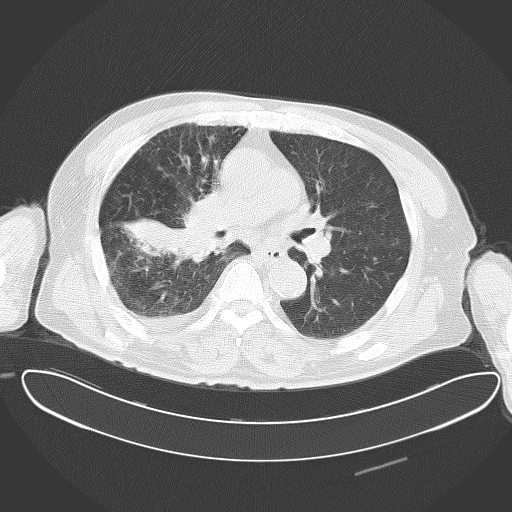
Chest CT, one axial slice. Slice 33 of 62 in the series (ordered by position). 120 kVp. Lung window (W 1500 / L -600 HU). 5 mm slice thickness. 512 × 512 image matrix. Patient: male, 78 years. Case-level facts recorded for this patient, not image findings: clinical TNM (as recorded): T2 N1 M1.
Annotated regions visible in this slice (bounding box drawn by a radiologist):
- lung tumour (recorded histology: adenocarcinoma): bounding box <117,192,225,274> (left, top, right, bottom; pixels)